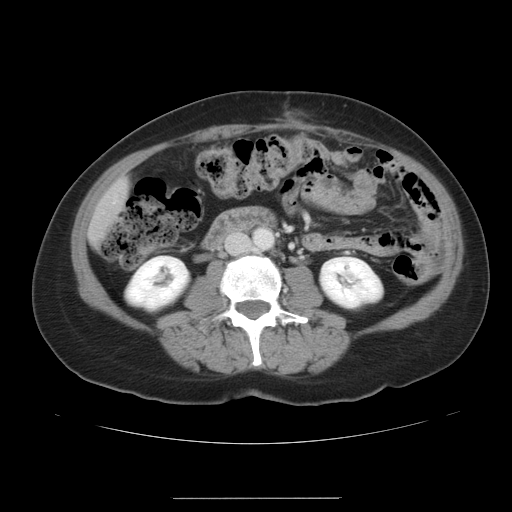
Contrast-enhanced abdominal CT, one axial slice. Slice 8 of 41 in the series (ordered by position). 120 kVp. Intravenous contrast given. Soft-tissue window (W 400 / L 40 HU). 5 mm slice thickness. 512 × 512 image matrix, field of view 381 × 381 mm. Female patient, age 63 years. From the clinical record (not read from this slice): diagnosis: colorectal cancer liver metastases, imaged before liver resection.
Annotated regions visible in this slice (expert manual segmentation):
- liver: bounding box [x1, y1, x2, y2] px = [91, 182, 129, 241]
- planned liver remnant (the part of the liver to remain after resection): [91, 182, 129, 240]